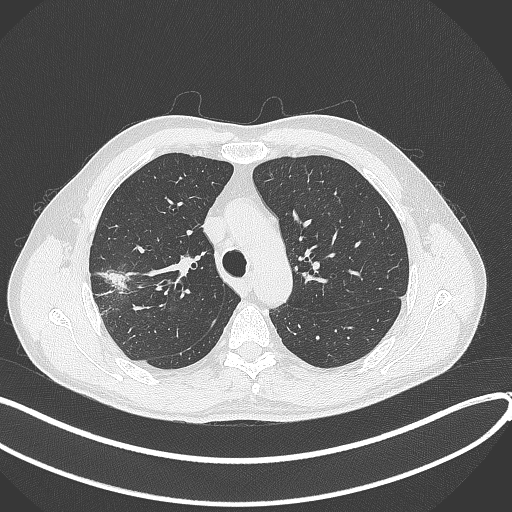
Chest CT, one axial slice. Position 302 of 381 along the scan axis. Reconstruction kernel B70f. 120 kVp. Lung window (W 1500 / L -600 HU). 512 × 512 image matrix, field of view 400 × 400 mm. Male patient, age 62 years. Case-level facts recorded for this patient, not image findings: clinical TNM (as recorded): T1c N0 M0.
Annotated regions visible in this slice (rectangle marked by the reading radiologist):
- lung tumour (recorded histology: adenocarcinoma): box from (x=99, y=268) to (x=132, y=297) px